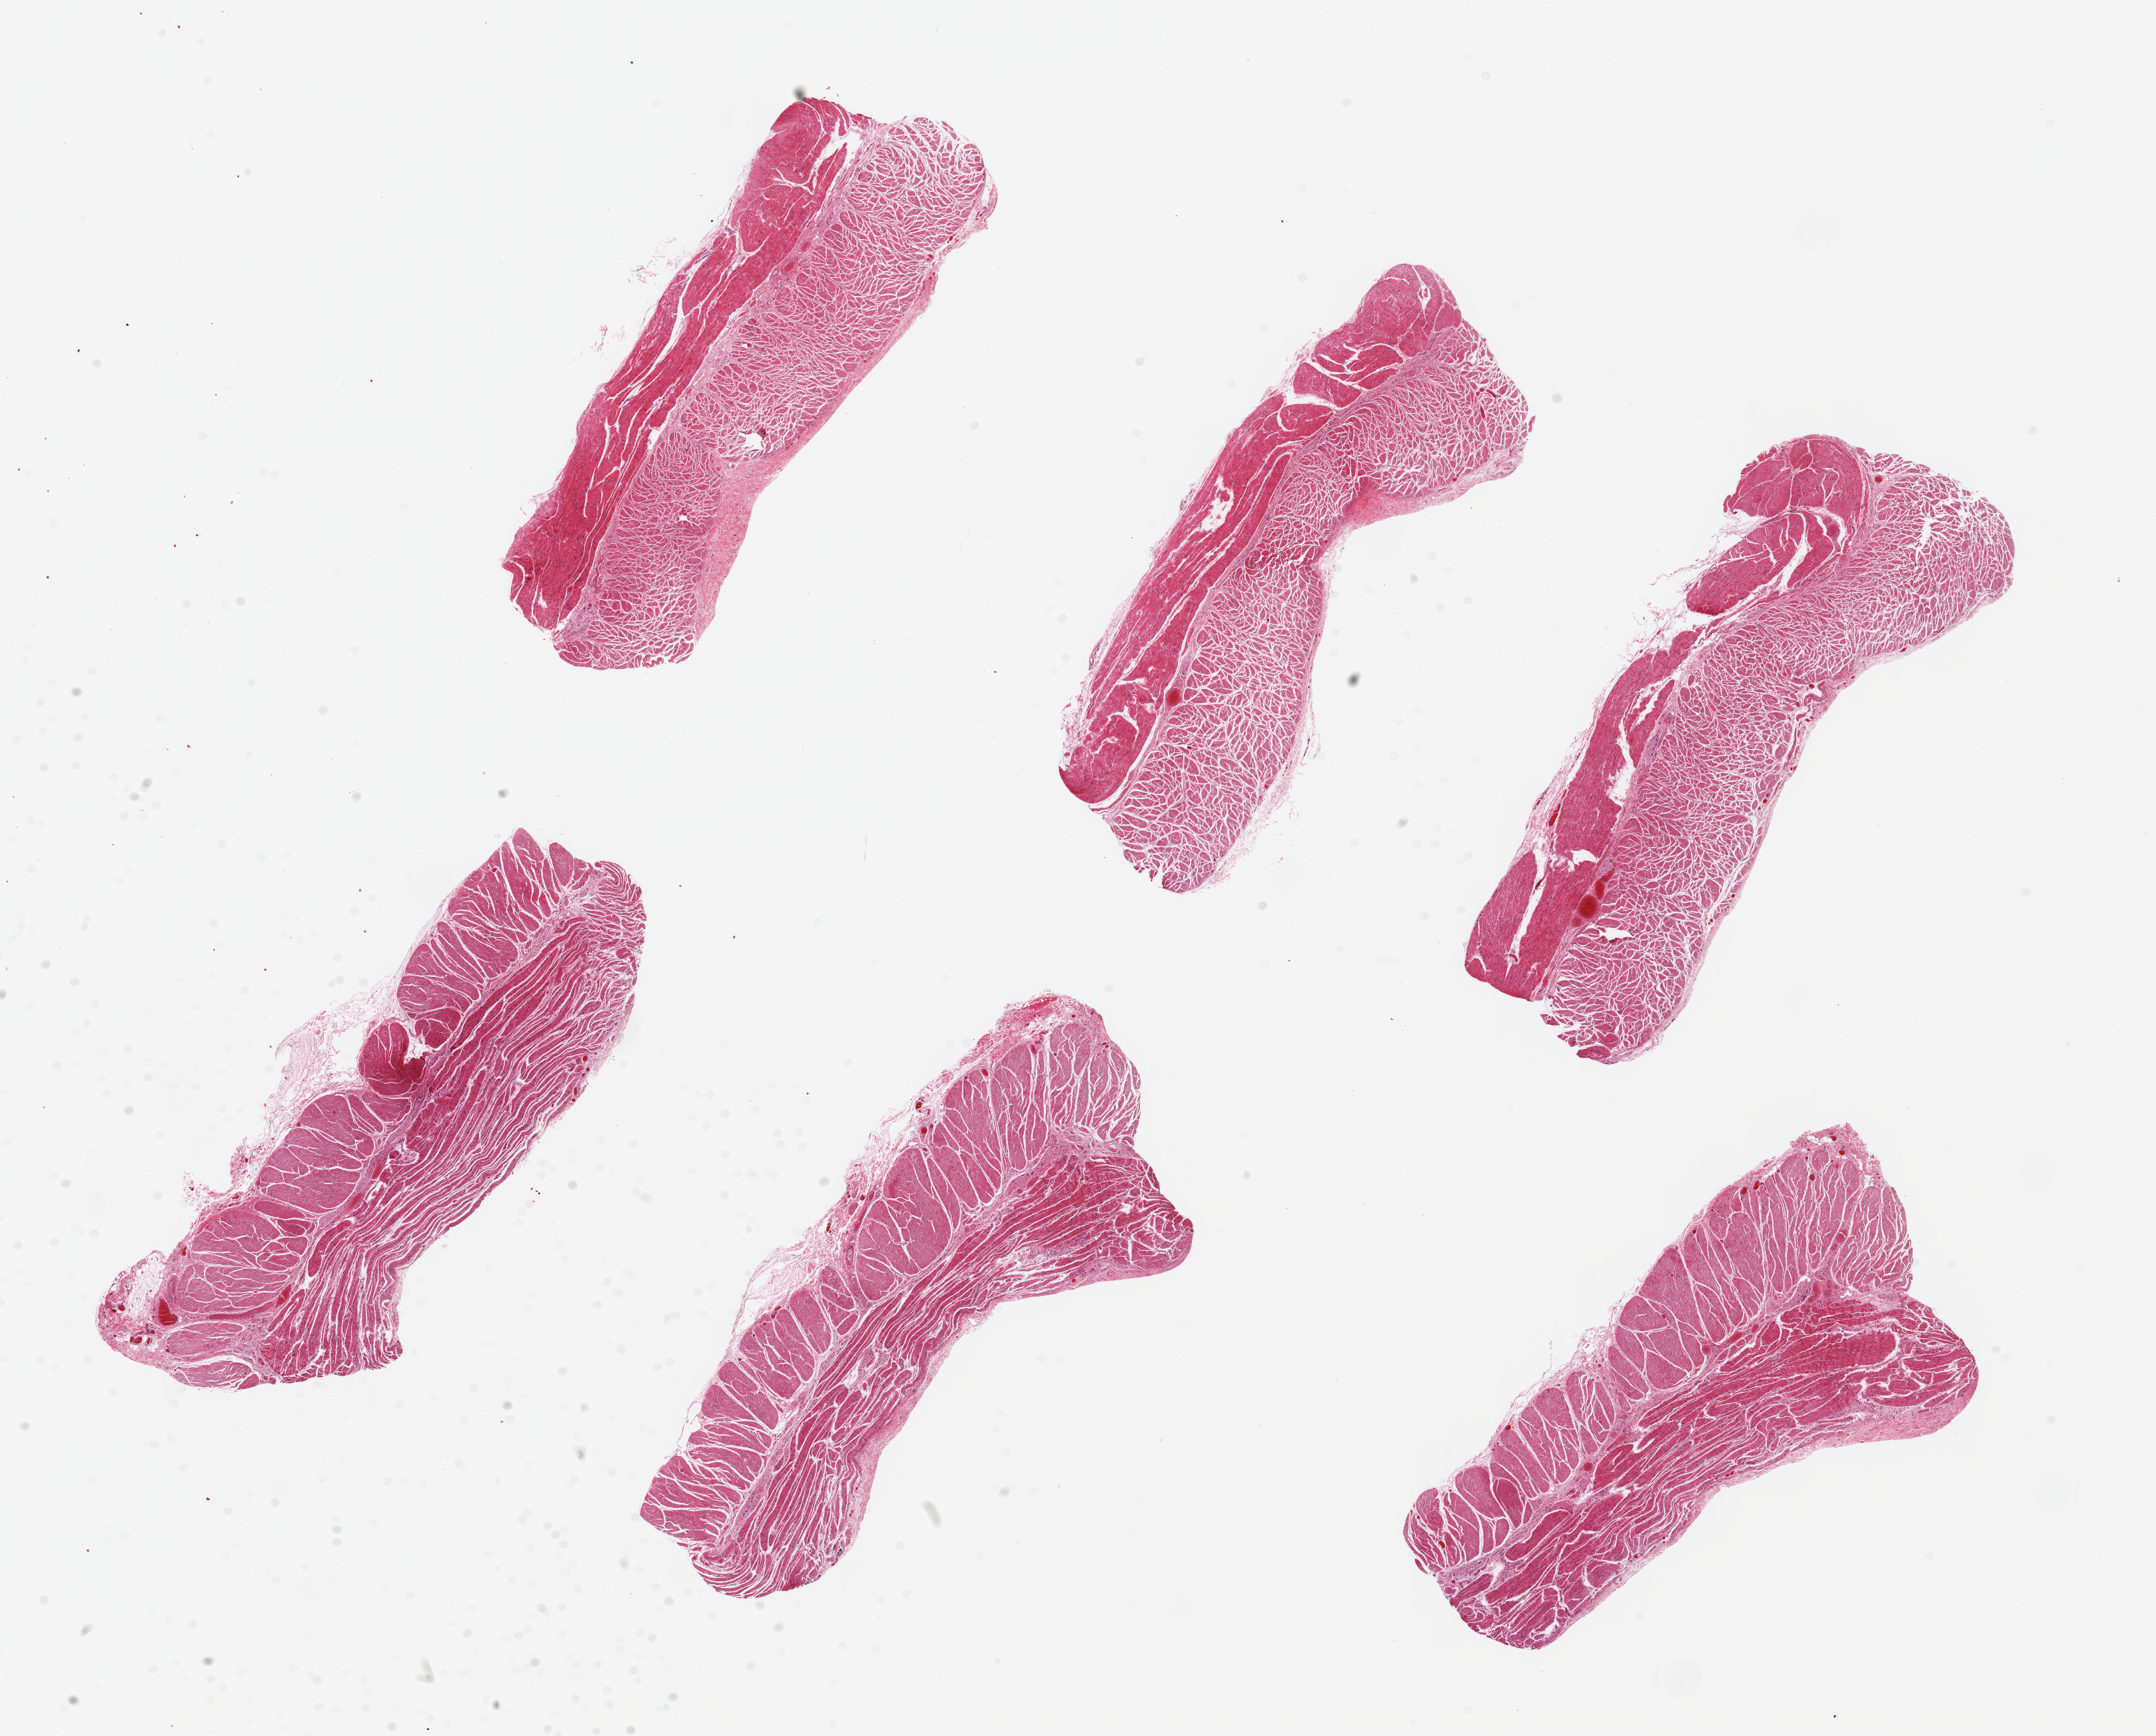
Hematoxylin and eosin (H&E) whole-slide image — whole scanned area (about 25.6 x 20.6 mm, slide scanned at 20x) shown as a low-resolution overview; PAXgene-fixed, paraffin-embedded tissue; section of esophageal muscle (target tissue); tissue donor sample.
Reviewer comment on this tissue sample: 6 pieces, up to 8x4mm; Well dissected muscle.